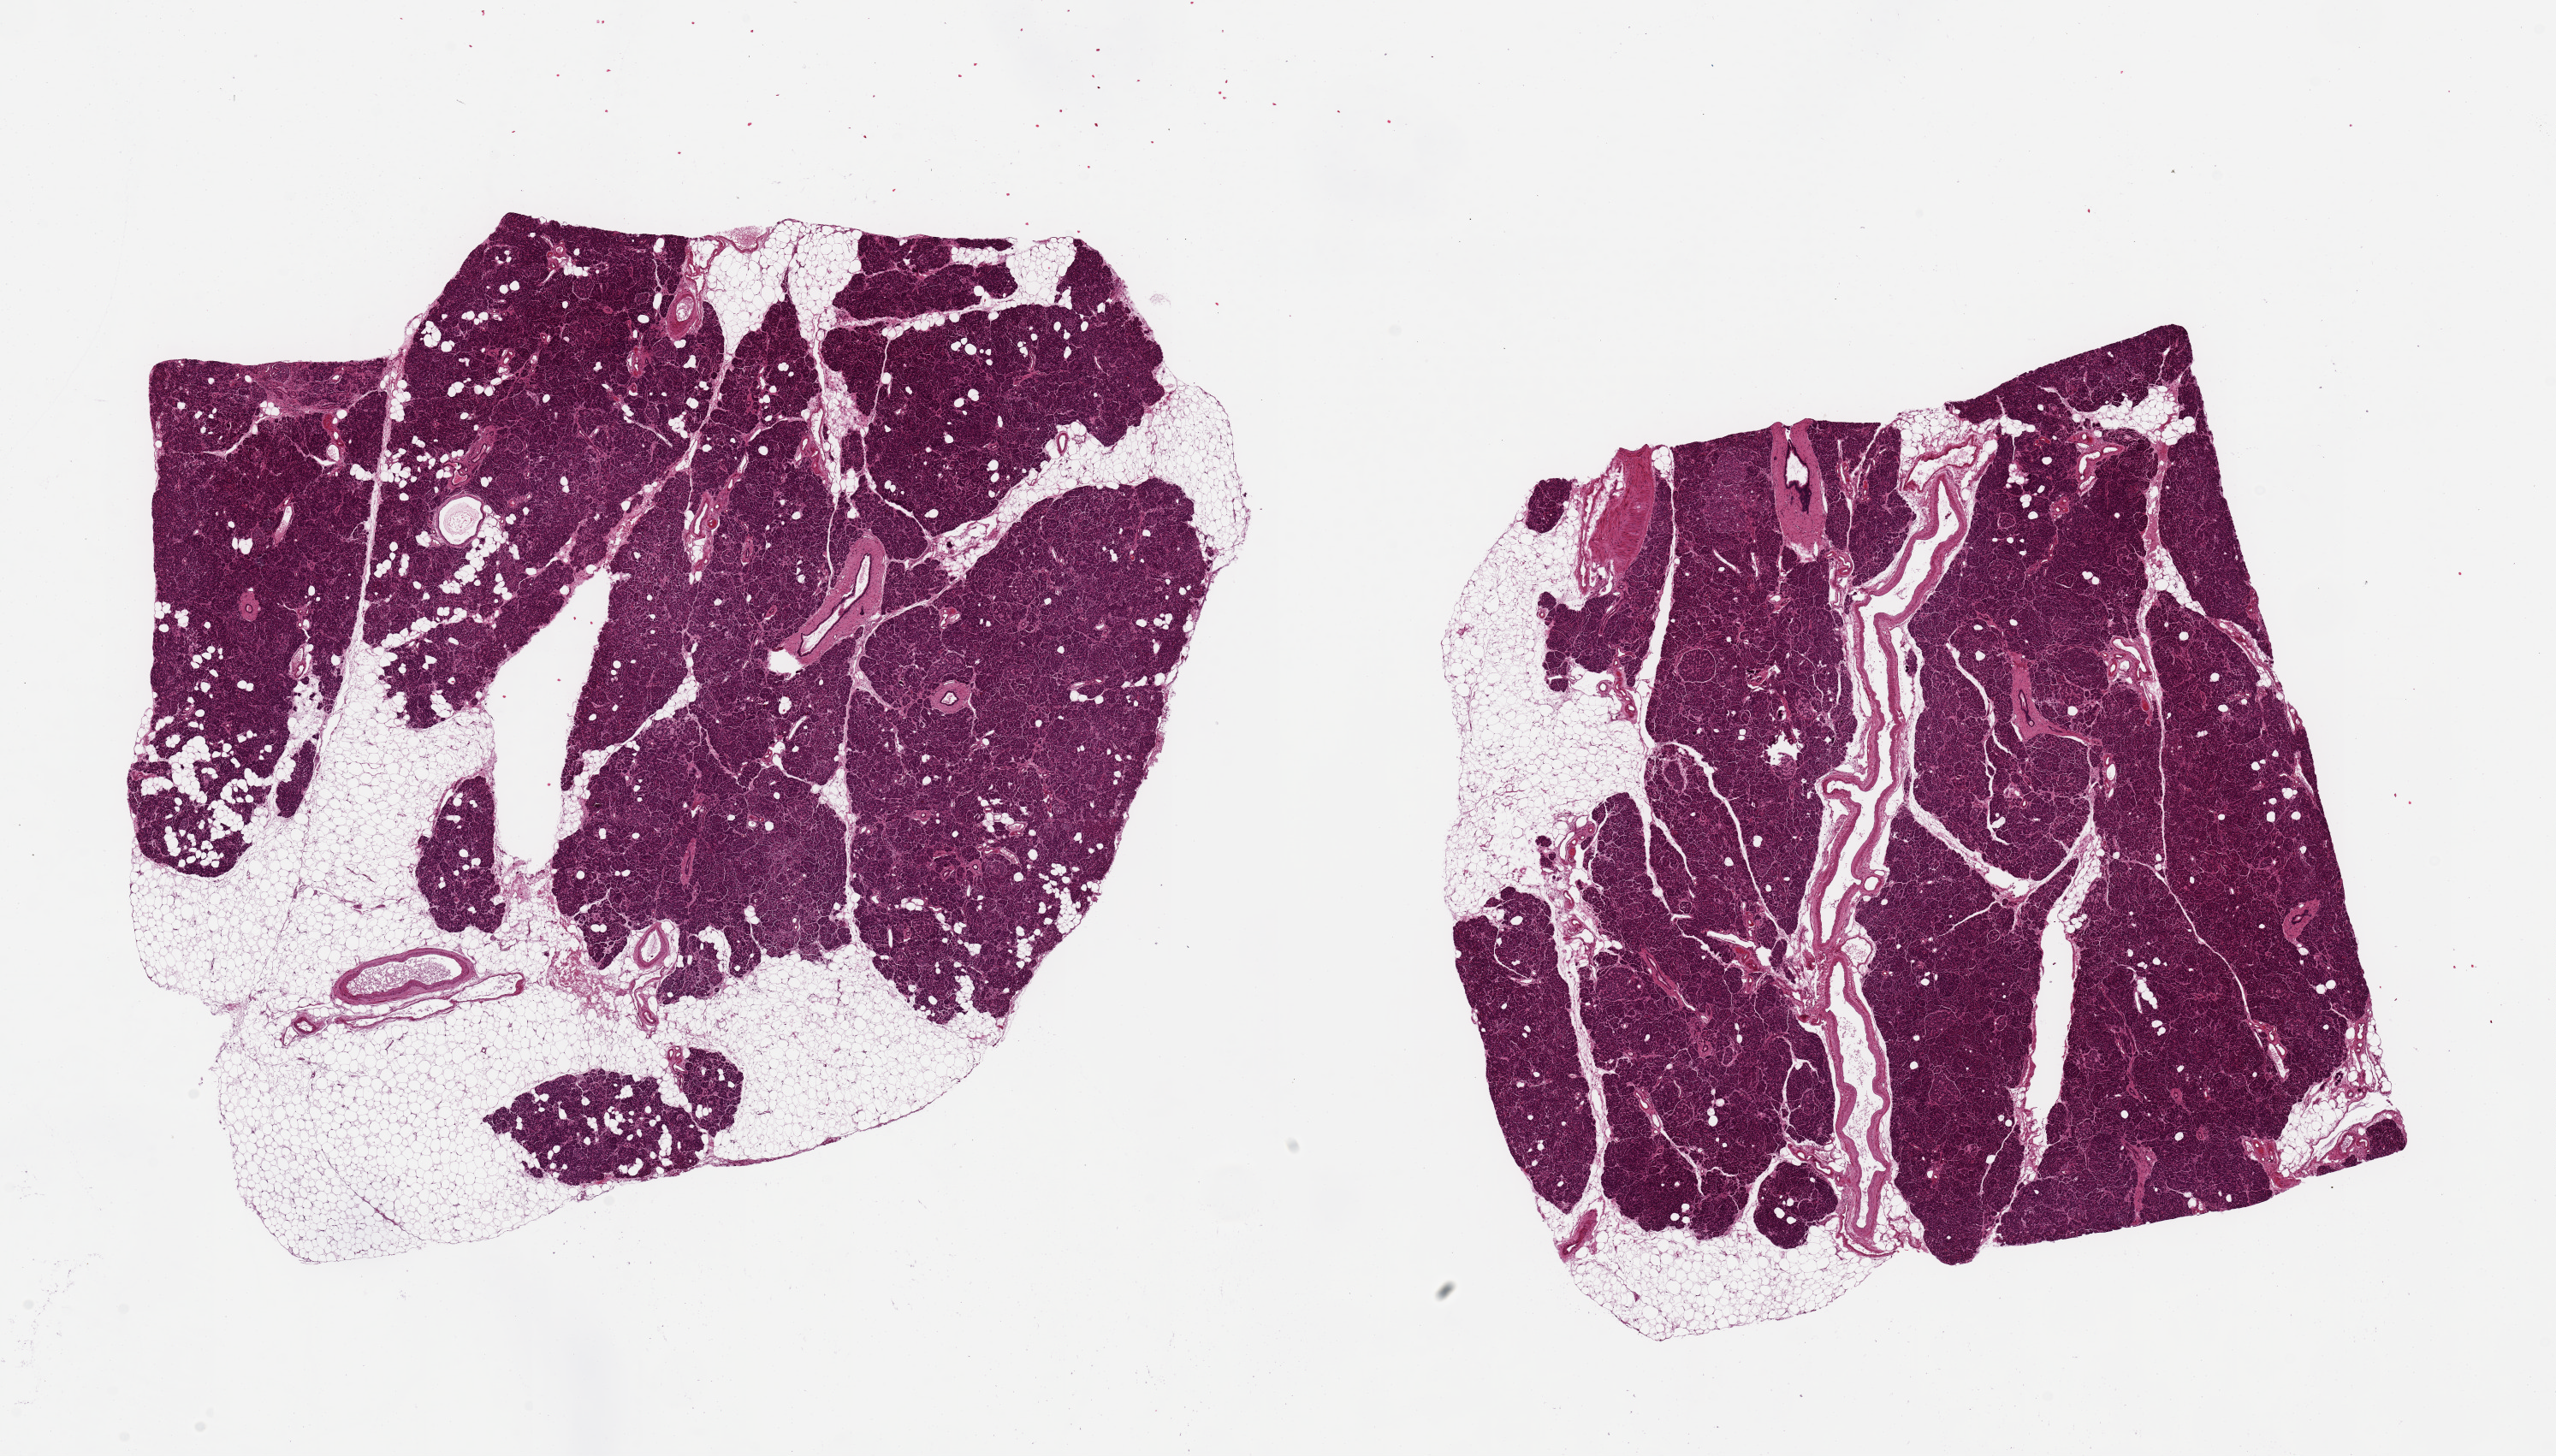
Whole-slide image, haematoxylin and eosin stain, low-resolution overview of the scanned area, about 23.6 x 13.5 mm; PAXgene-fixed, paraffin-embedded tissue; section of pancreas (target tissue); tissue donor sample. Donor sex: female.
Pathologist's review note for this sample: 2 pieces, 8x8 & 10x8 mm, 10-20% embedded fat.